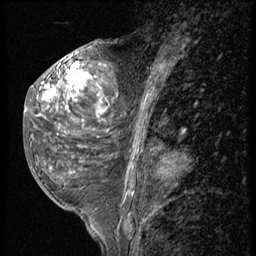
Breast MRI (dynamic contrast-enhanced), one sagittal slice; position 25 of 56 along the scan axis; 3 images stored at this slice position (order not interpretable as contrast timing); 1.5 T; TE 4.2 ms, TR 9 ms; 2.5 mm slice thickness; 256 × 256 image matrix, field of view 180 × 180 mm. Patient: female, 50 years. From the clinical record (not read from this slice): setting: breast cancer imaged before/during neoadjuvant chemotherapy; receptor status: triple-negative.
Structures marked on this image (semi-automatically segmented with operator editing):
- analysis volume of interest (the breast-tissue region the enhancement analysis was run in; not a lesion): bounding box (x1, y1, x2, y2) in pixels: (25, 50, 117, 191)
- tumour enhancement mask (voxels above the 140 % enhancement threshold inside the analysis volume of interest): (41, 63, 107, 113)